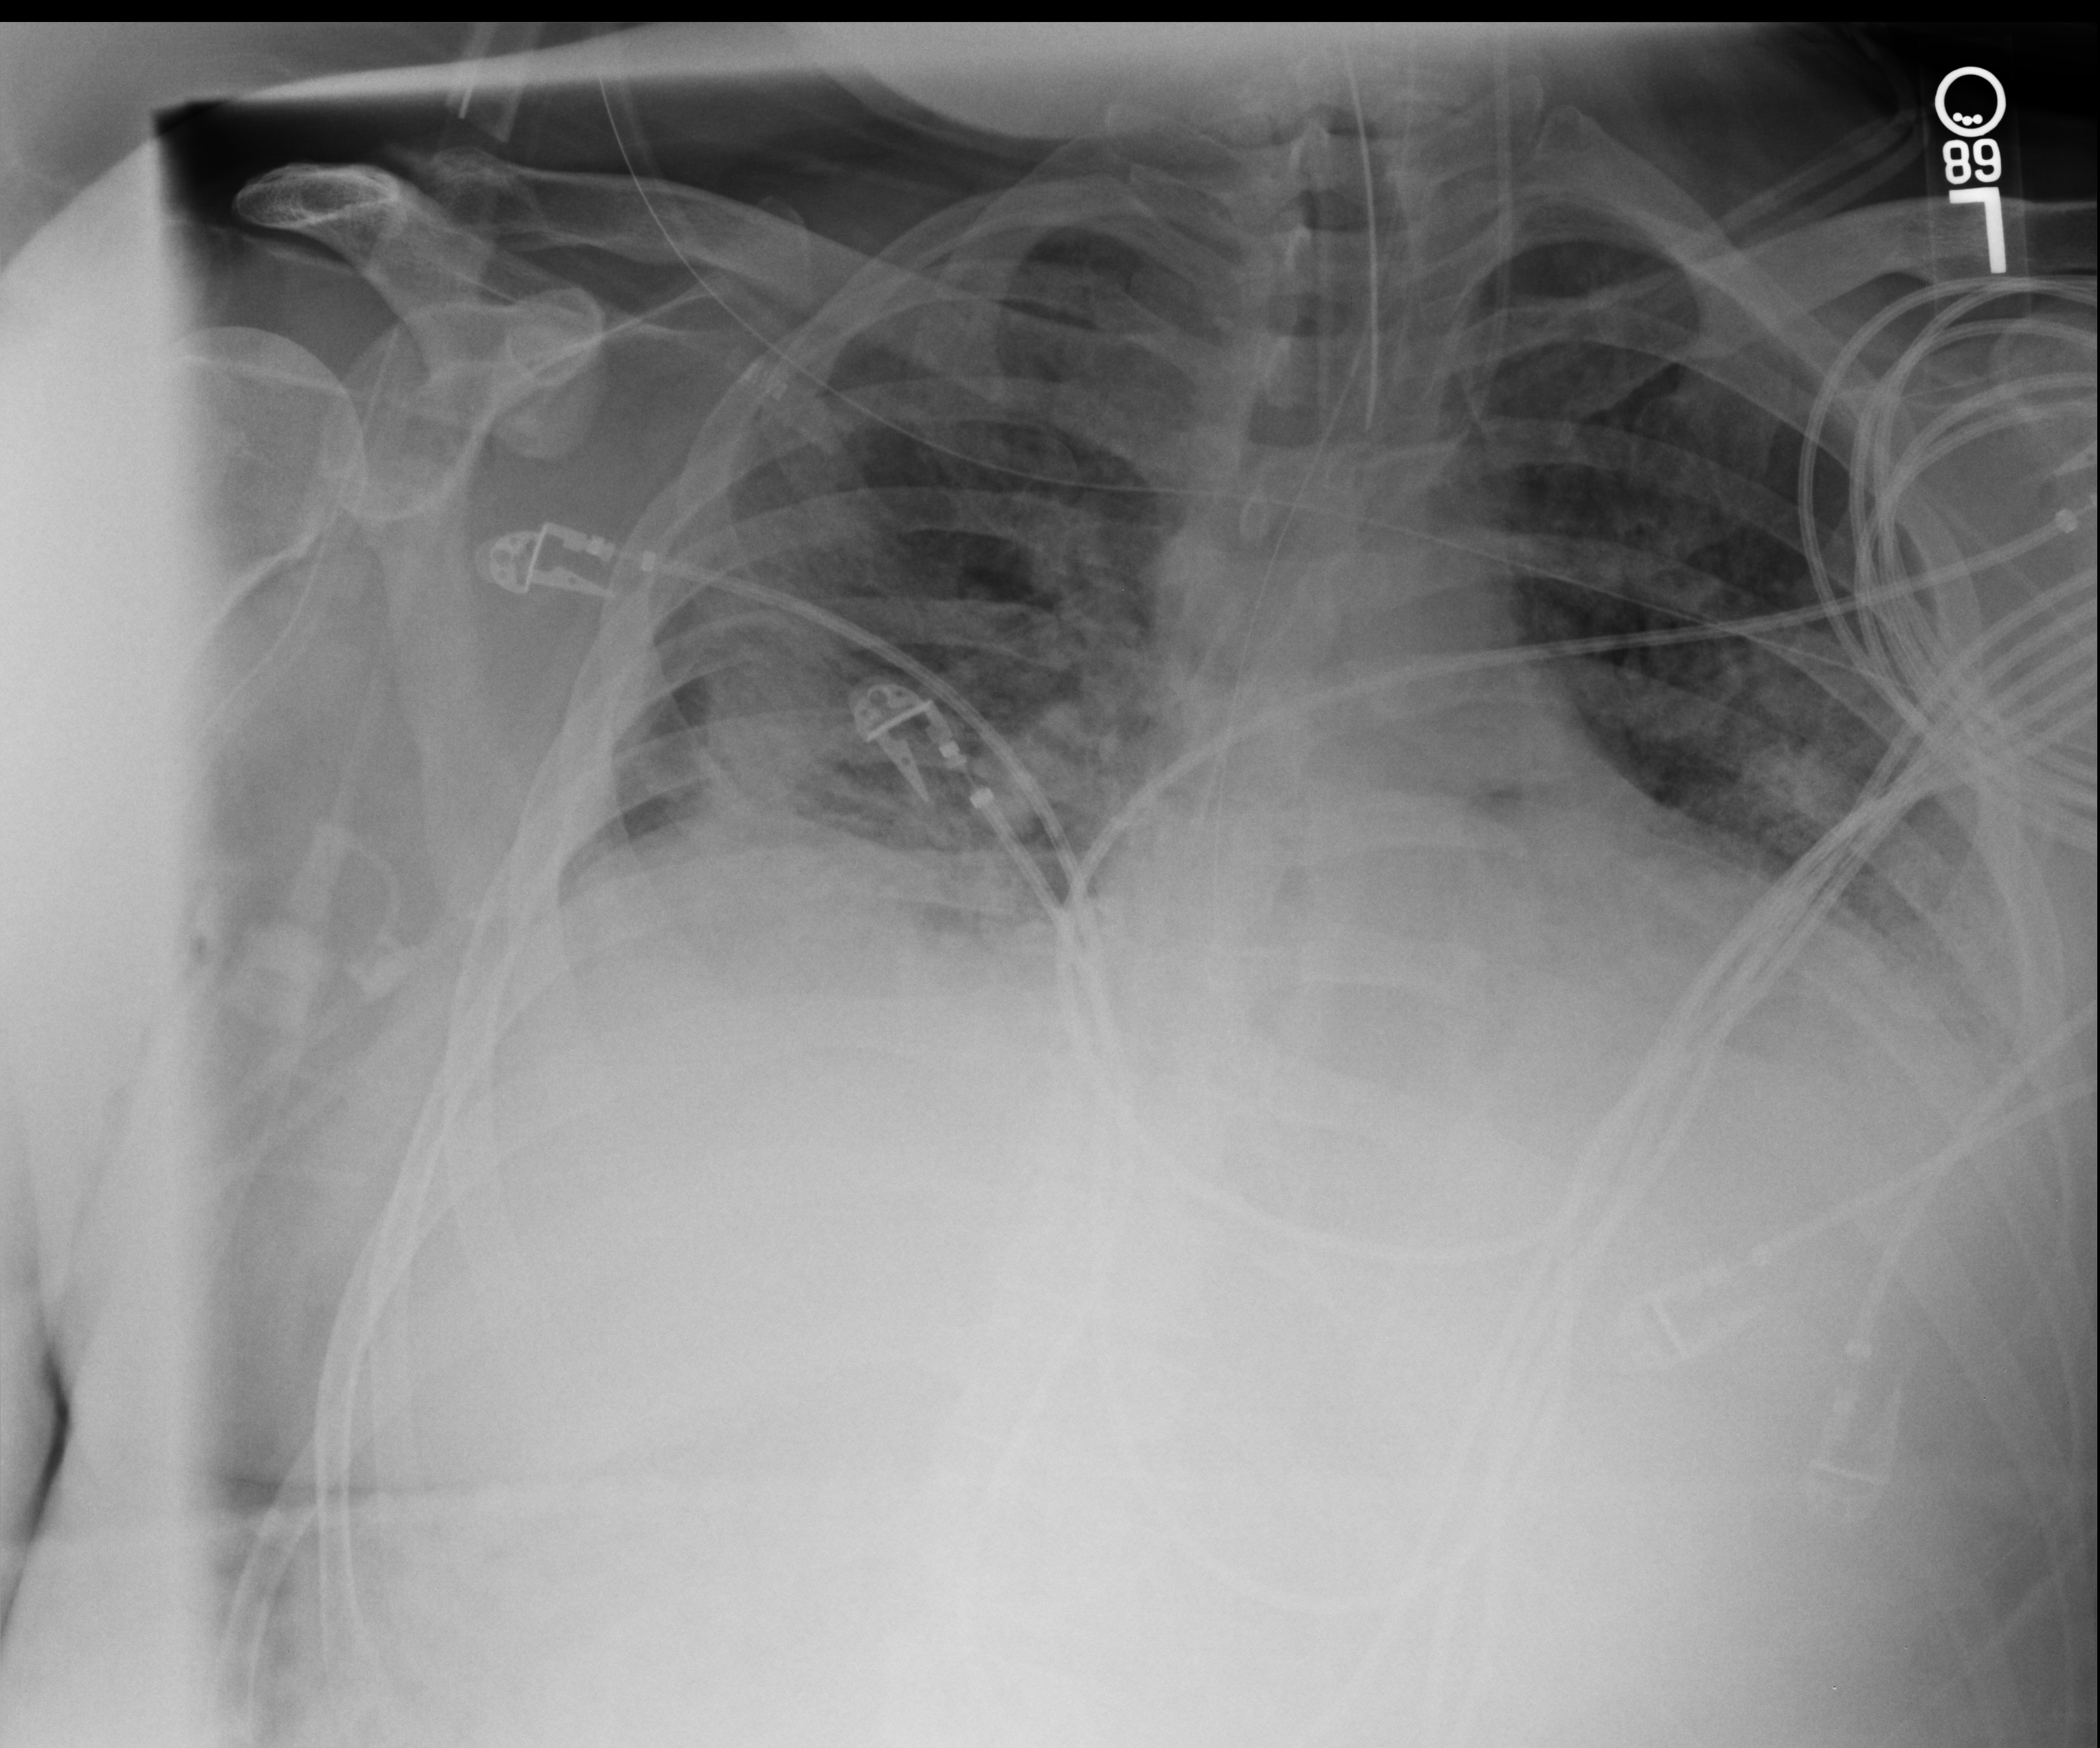
Bedside chest radiograph (computed radiography), anteroposterior (AP) projection. Patient hospitalised with COVID-19; male, aged 18–59 years.
Admission-level facts for this patient (not findings on this image; timing relative to this image not recorded):
- mechanically ventilated during this hospital stay: yes